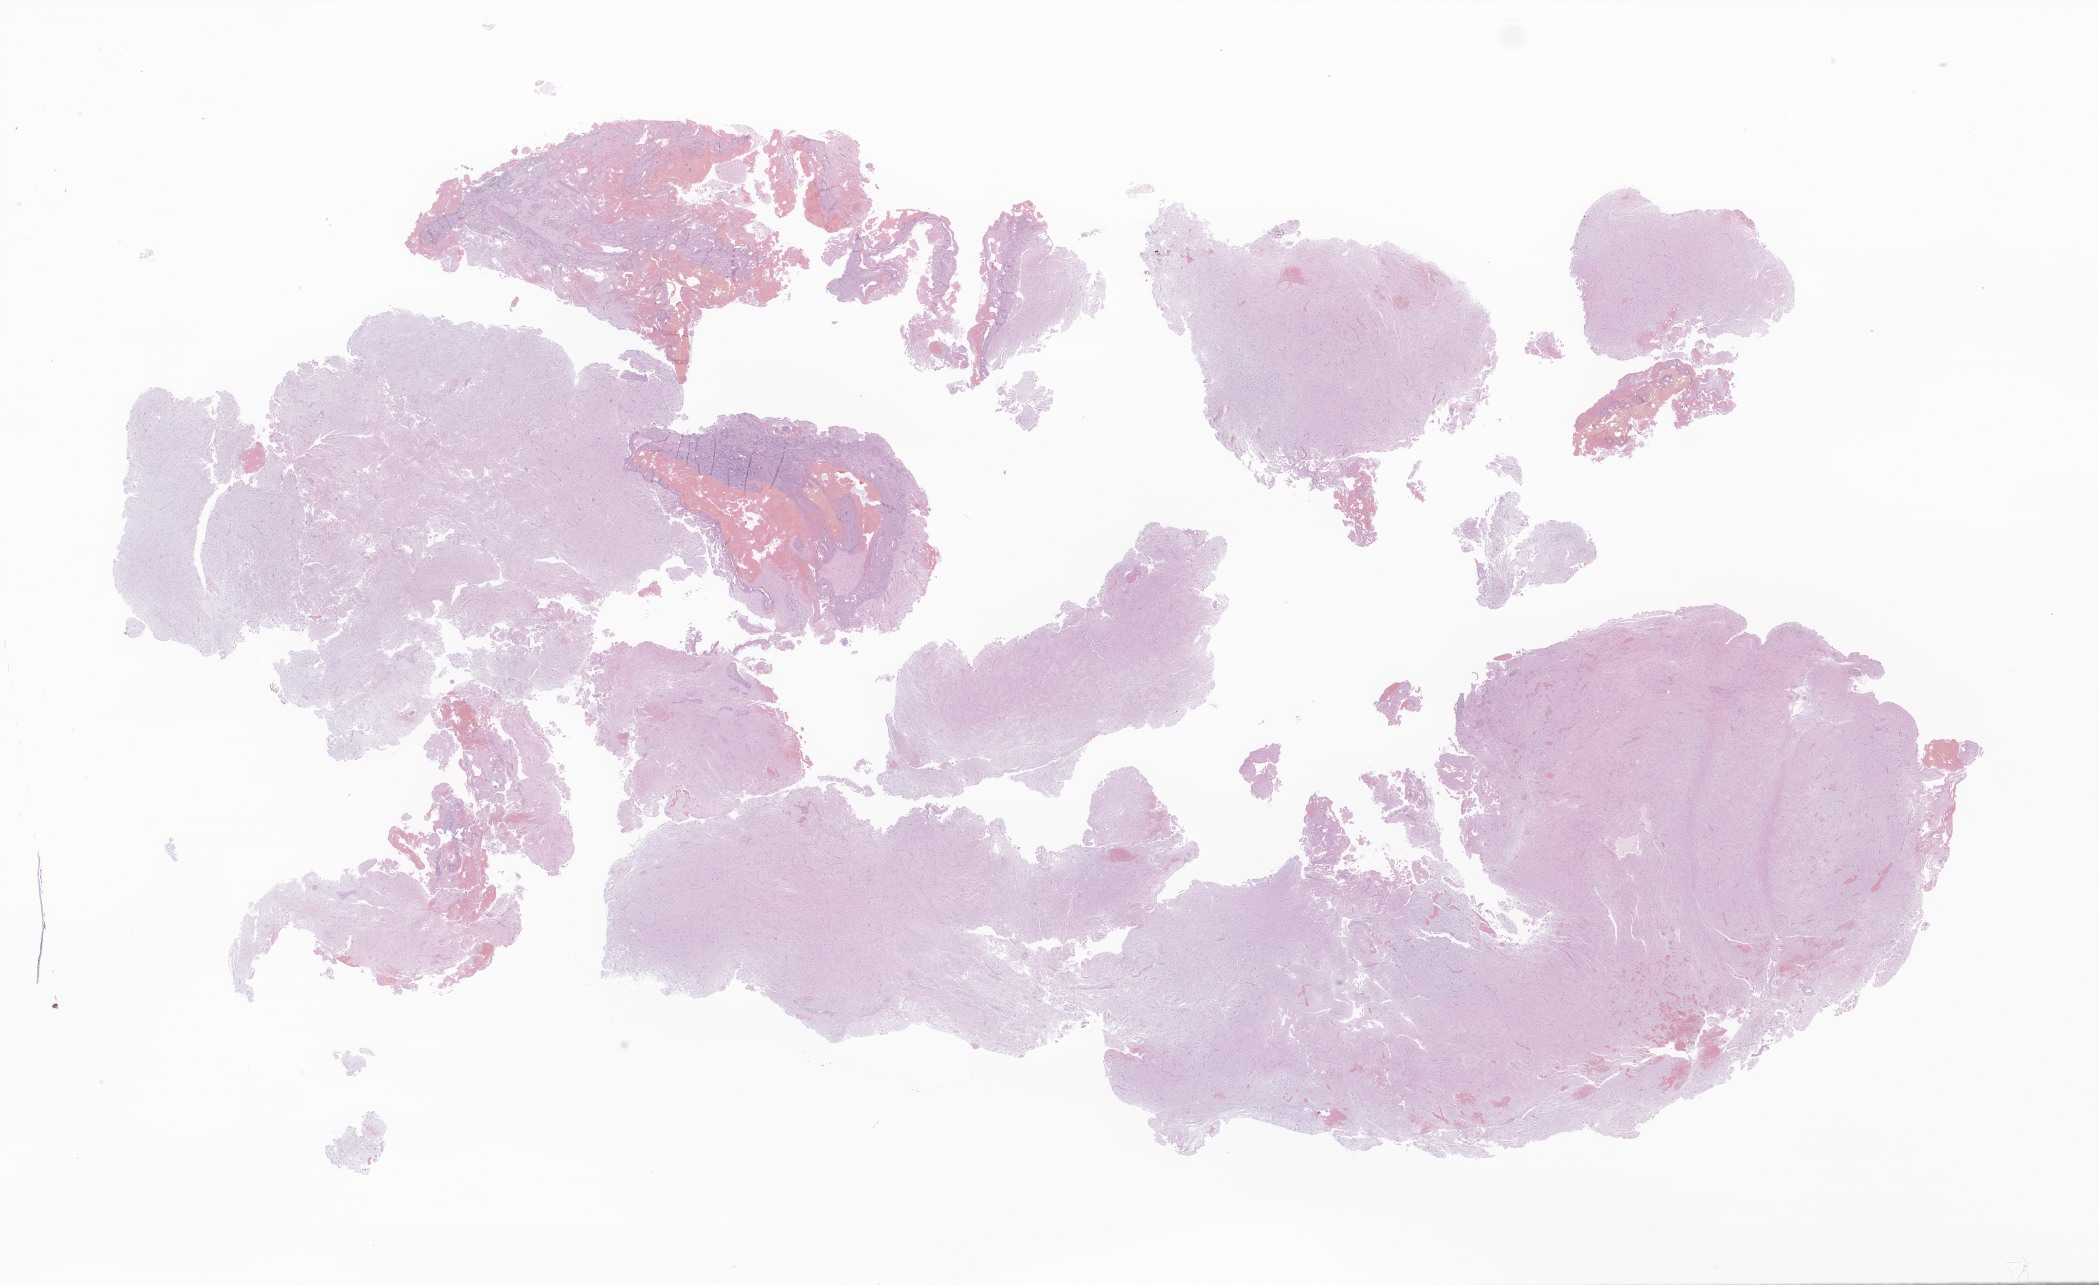
Hematoxylin and eosin (H&E) whole-slide image of tumor tissue from the cerebral ventricle — shown as a low-resolution overview of the whole scanned area (about 35.4 x 21.7 mm); FFPE section. Patient female; age 140 months (11 years 8 months).
Diagnosis: Pilocytic astrocytoma.